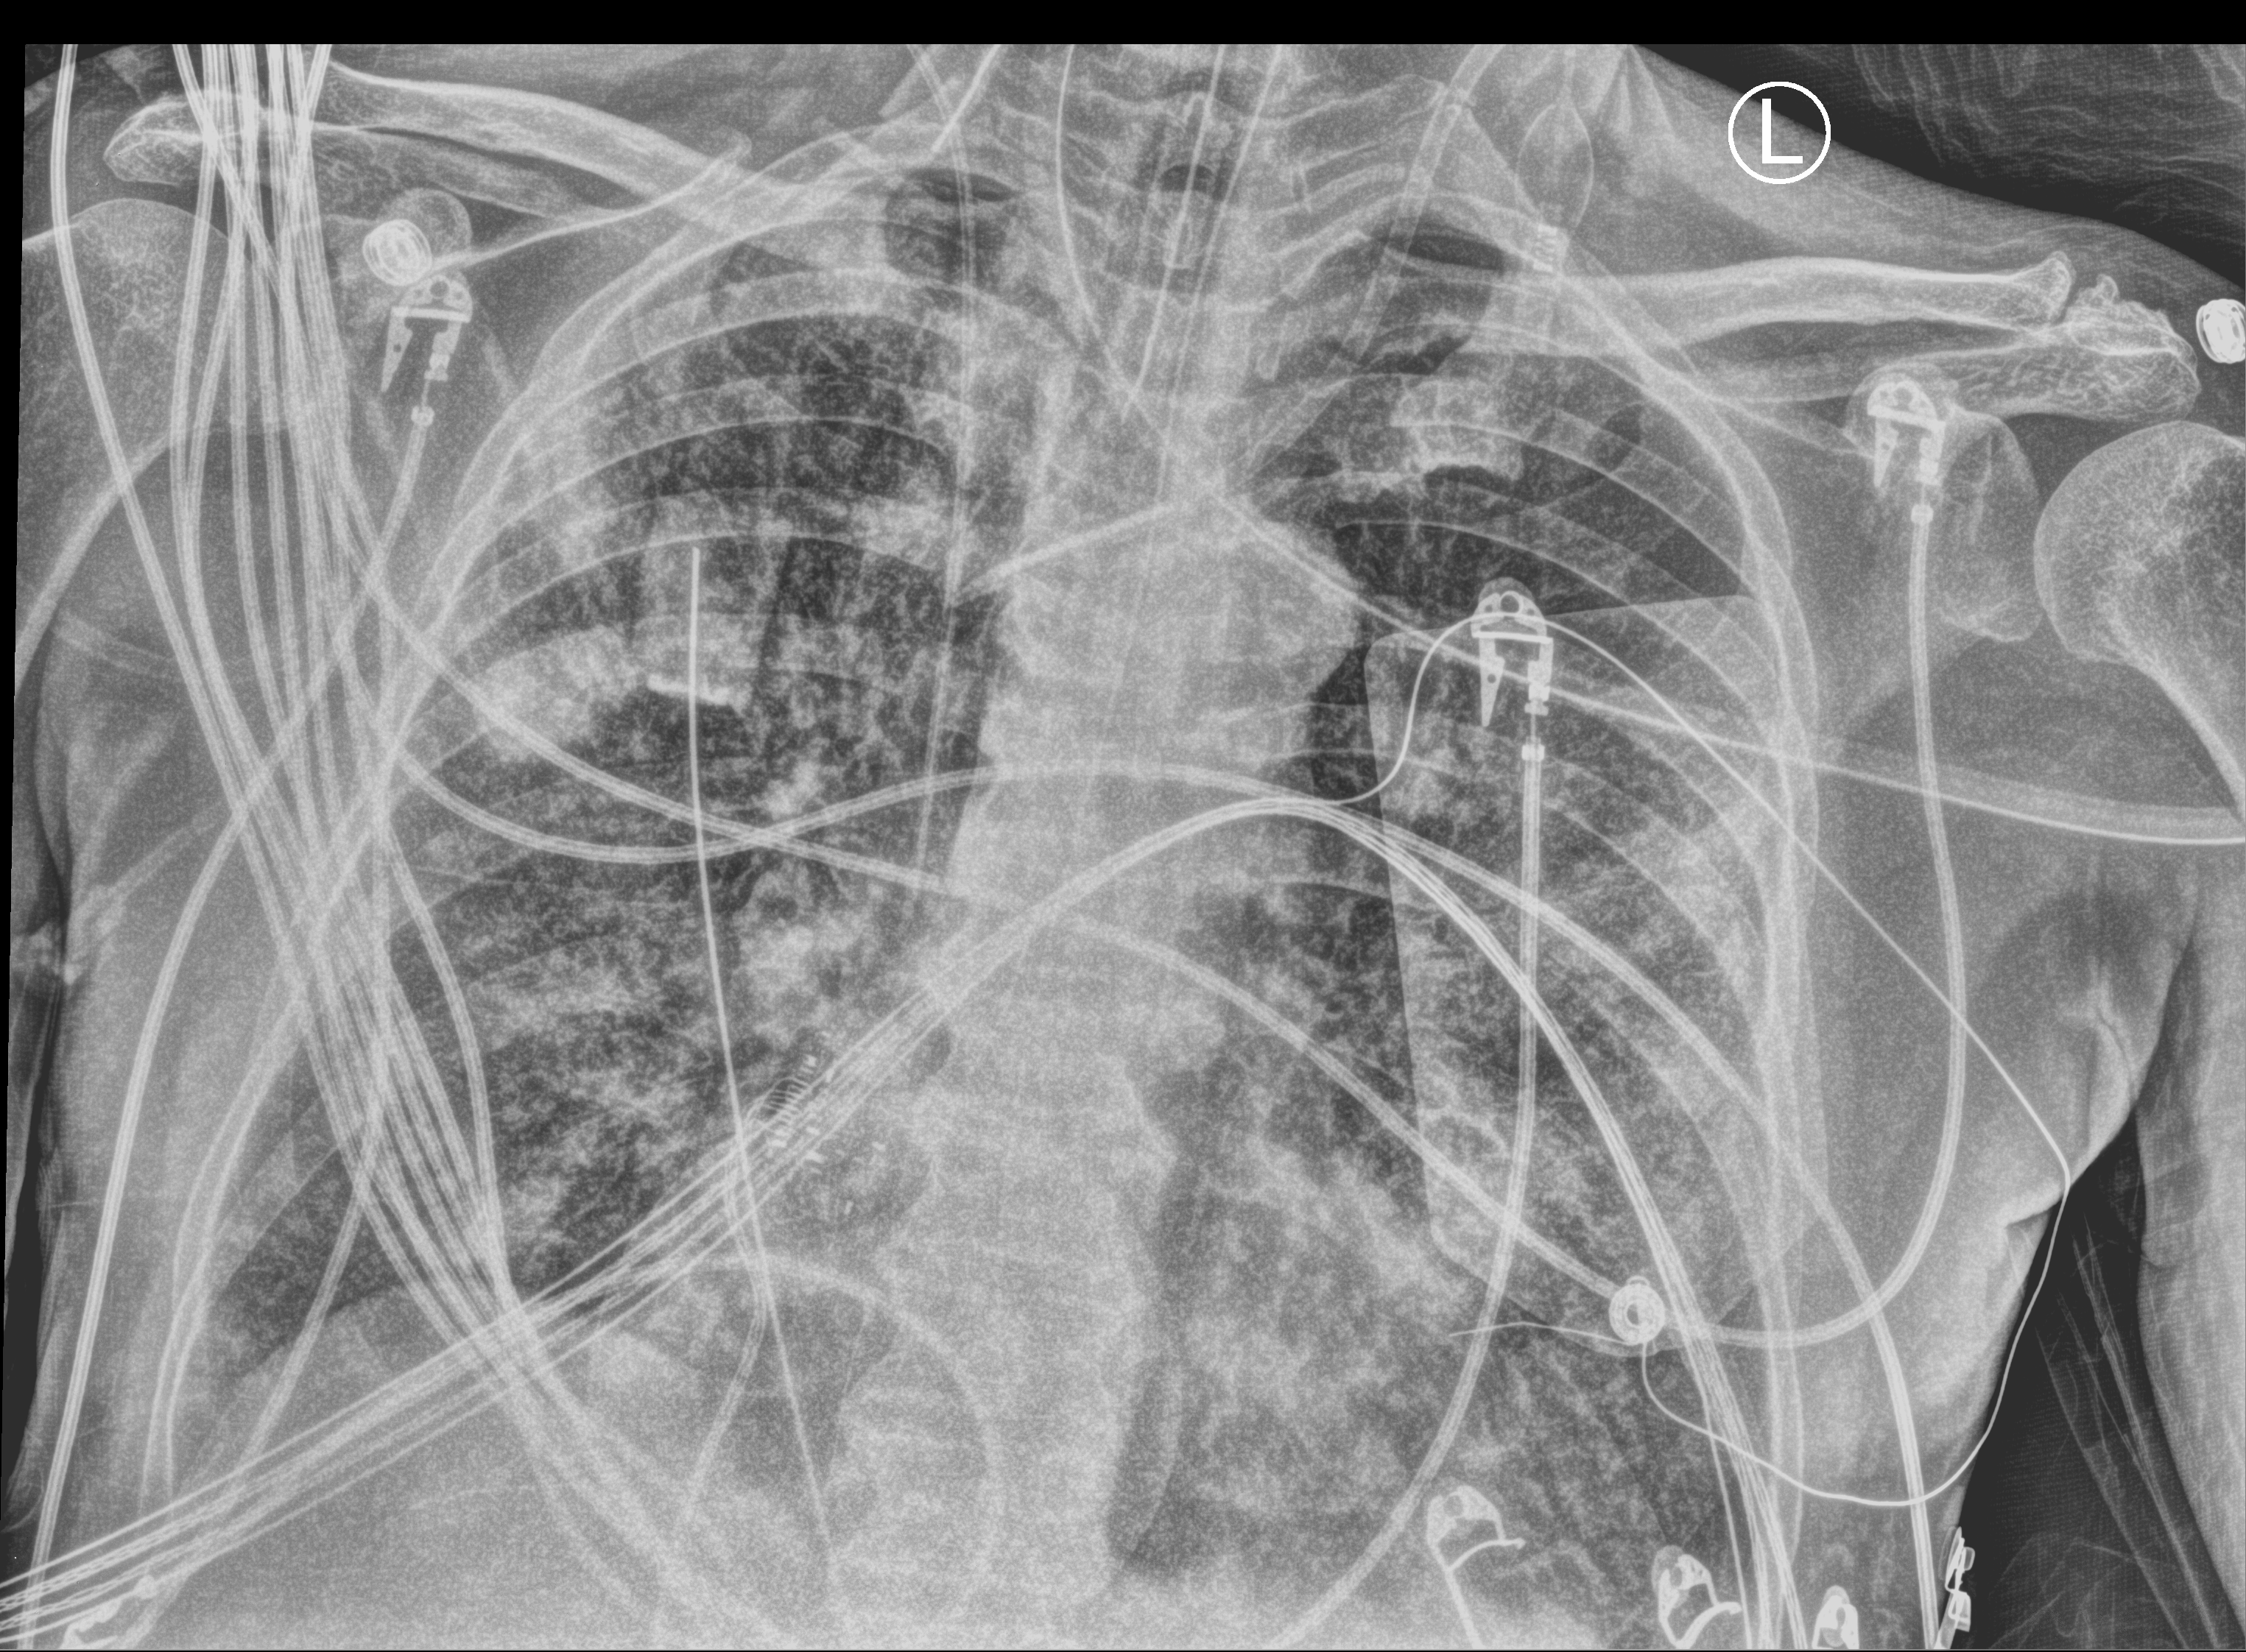
Bedside chest radiograph (computed radiography); anteroposterior (AP) projection. Patient hospitalised with COVID-19; male, aged 60–74 years.
Hospital-stay facts (about this admission, not read from this image; timing relative to this image not recorded): length of hospital stay: 26 days; admitted to intensive care during this hospital stay: yes.